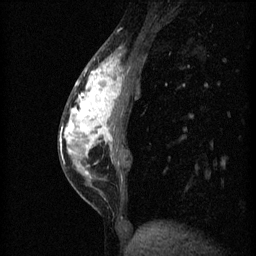
Breast MRI (dynamic contrast-enhanced), one sagittal slice. Slice 19 of 60 in the series (ordered by position). 3 images stored at this slice position (order not interpretable as contrast timing). 1.5 T. TE 4.2 ms, TR 11 ms. 256 × 256 image matrix, field of view 180 × 180 mm. Patient: female, 40 years.
Outlined on this slice (semi-automatic segmentation, software-assisted and operator-edited):
- analysis volume of interest (the breast-tissue region the enhancement analysis was run in; not a lesion): bounding box (x1, y1, x2, y2) in pixels: (59, 42, 137, 203)
- tumour enhancement mask (voxels above the 70 % enhancement threshold inside the analysis volume of interest): (61, 56, 122, 175)